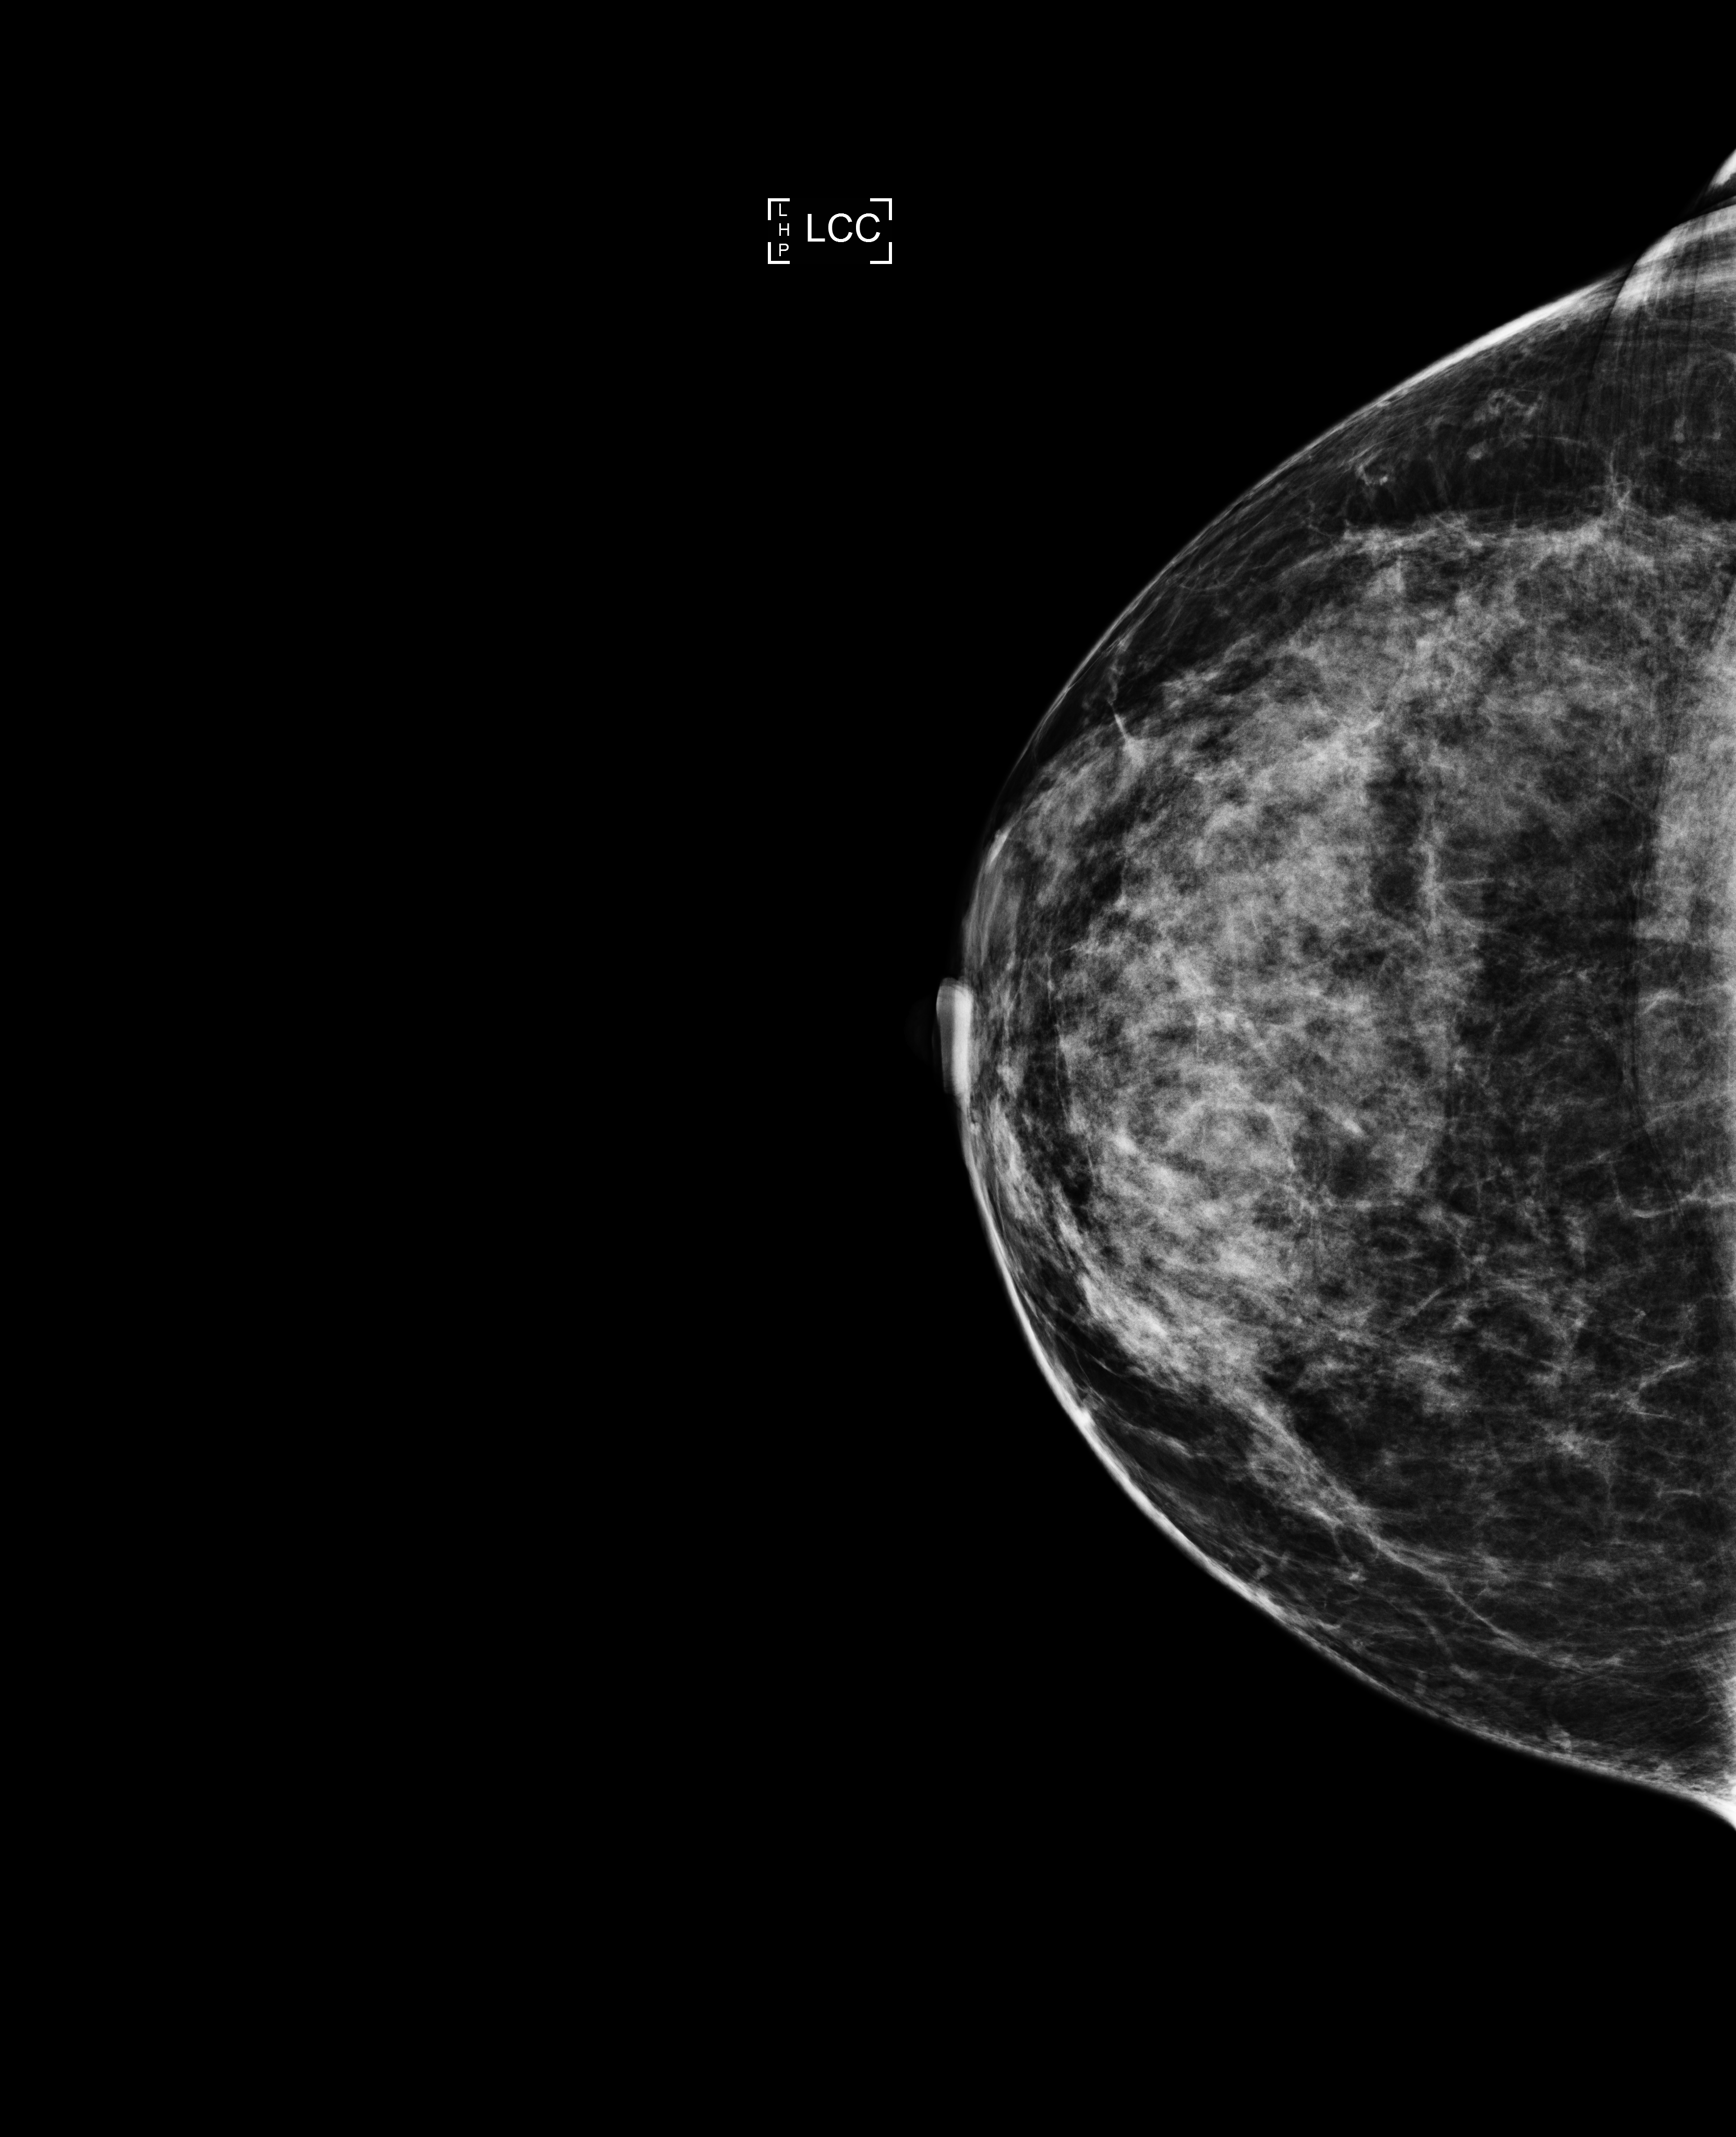
Annual screening mammography examination; system: Selenia Dimensions. Female patient, age 42 years.
Image type: full-field digital mammogram. Breast: left. Projection: craniocaudal (CC) view.